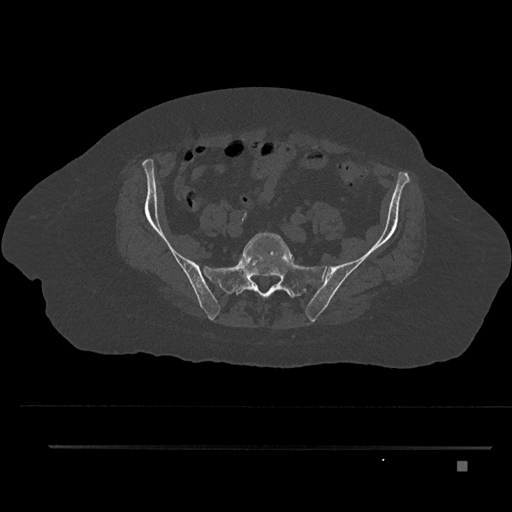
CT including the spine, one axial slice. Position 11 of 797 along the scan axis. 120 kVp. Bone window (W 1800 / L 400 HU). 512 × 512 image matrix, field of view 437 × 437 mm. Patient: female, 76 years. From the clinical record (not read from this slice): primary cancer: lung; vertebrae with lytic lesions (as recorded): T11, L3.
Annotated regions visible in this slice (semi-automatic segmentation, software-assisted and operator-edited):
- L5 vertebra: bounding box <243,232,291,293> (left, top, right, bottom; pixels)